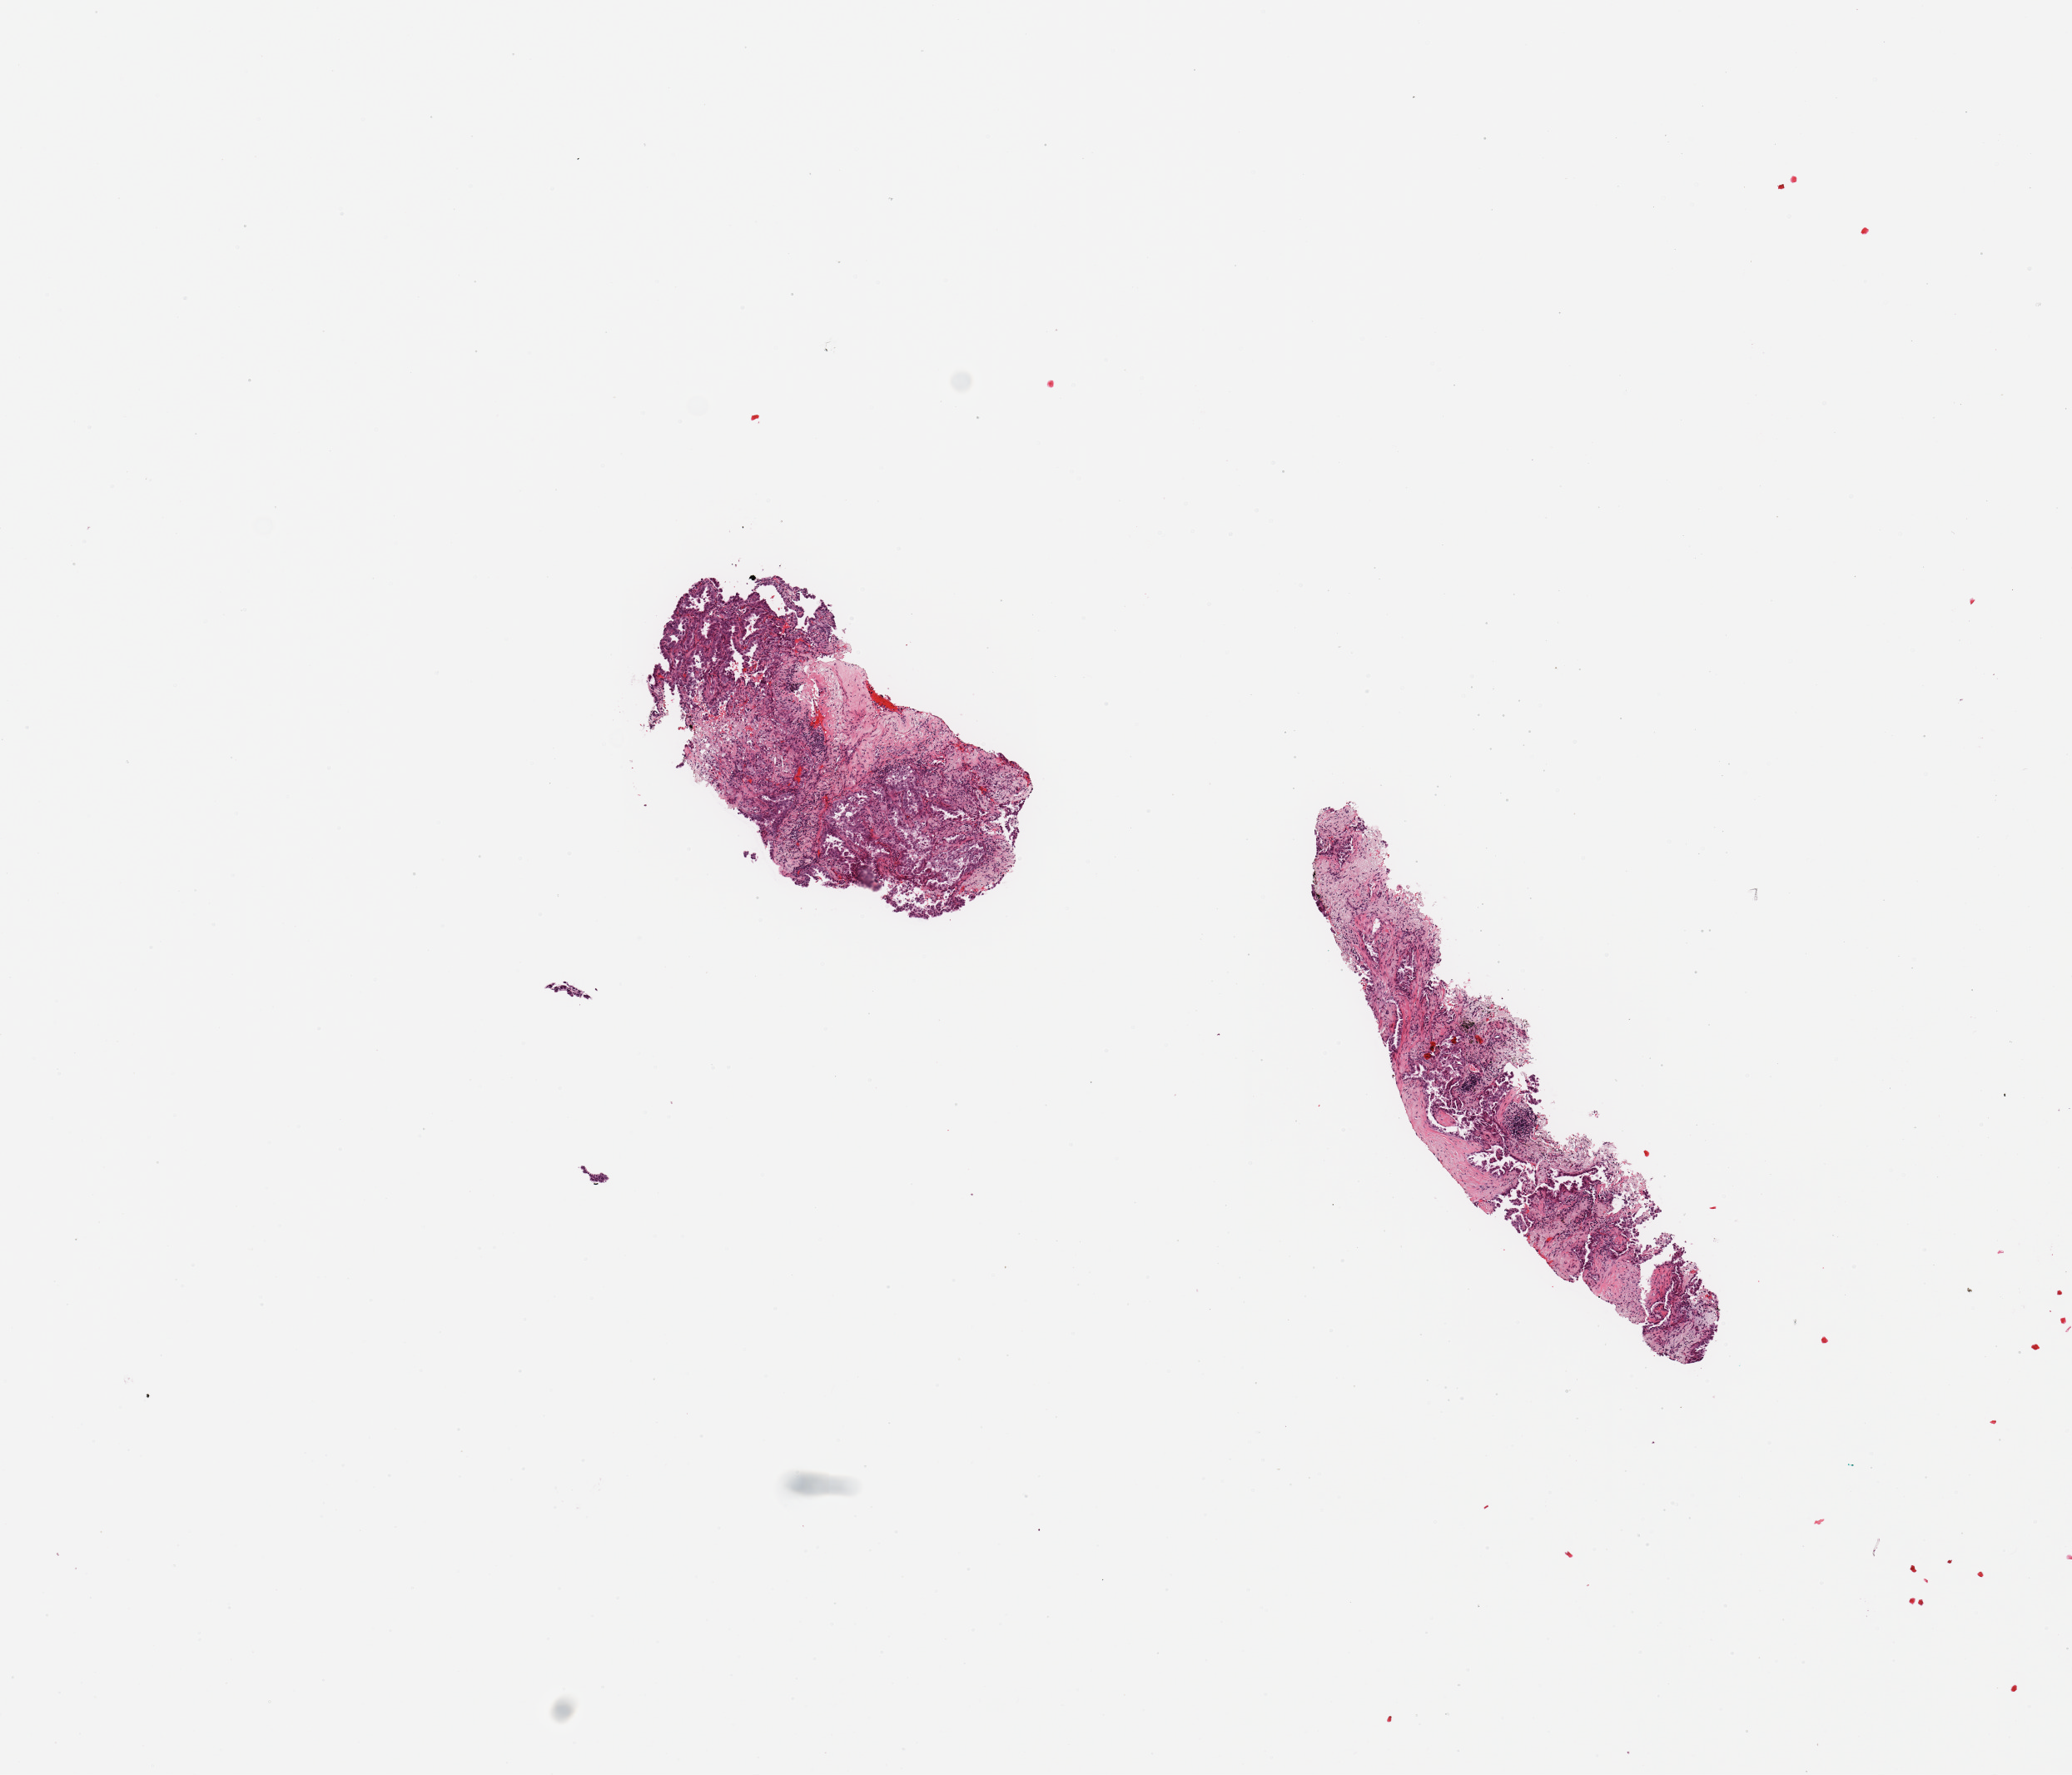
Digitized Hematoxylin and eosin (H&E) stained tissue section (whole slide), a low-resolution overview of the entire scanned area, about 9.8 x 8.4 mm (slide scanned at 20x), tumour tissue sample, sampled site: lung. Female, 65 y/o. Histologic grade: G2 (moderately differentiated). Composition of this section per pathologist review: tumour nuclei 80%, necrosis 5%.
Diagnosis: Adenocarcinoma, NOS. Primary tumour site (as recorded): left upper lobe. AJCC pathologic stage: IB.